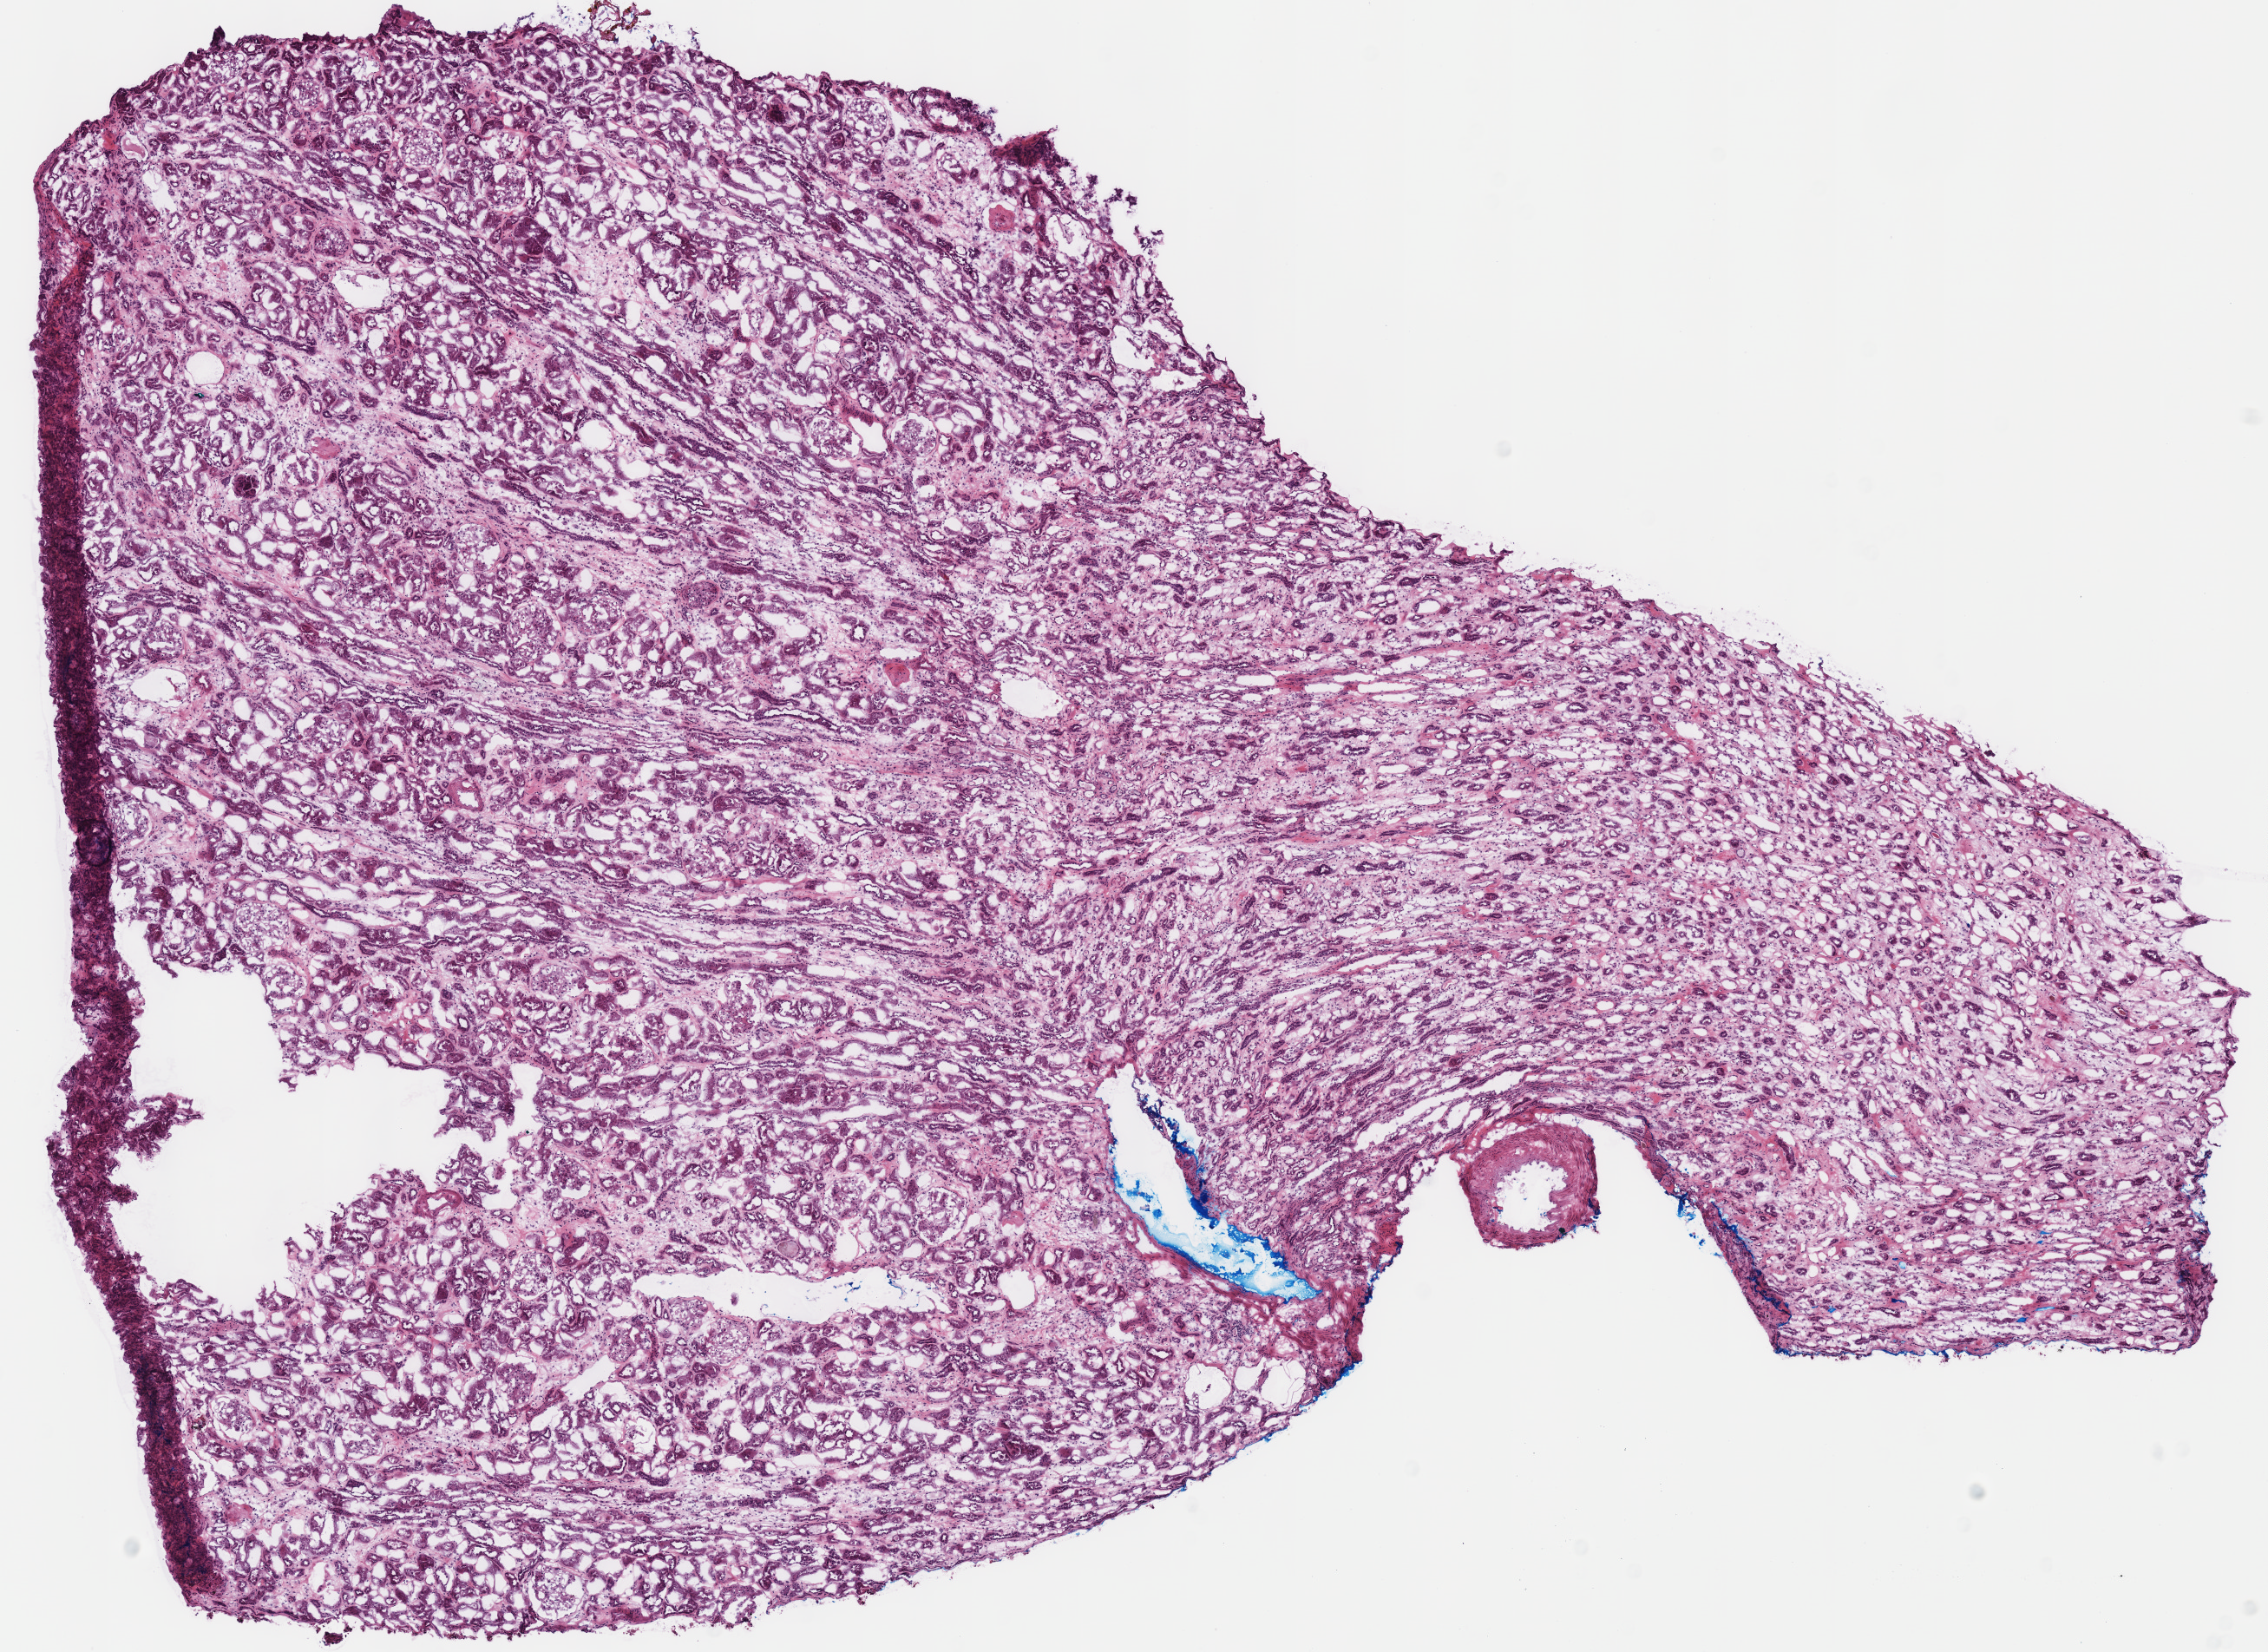
Digitized H&E tissue section (whole slide) — a low-resolution overview of the entire scanned area, about 10.3 x 7.5 mm (slide scanned at 40x), frozen section from the top of the tissue portion, kidney, solid tissue normal (non-tumour tissue) sample. Female patient; age at initial diagnosis 79 years. Composition of this section per pathologist review: tumour cells 0%, tumour nuclei 0%, normal cells 65%, stromal cells 35%, necrosis 0%. Infiltration values recorded for this section: lymphocyte infiltration 10%, monocyte infiltration 3%, neutrophil infiltration 0%.
* this section: solid tissue normal sample (biorepository sample class)
* patient diagnosis: Renal cell carcinoma, chromophobe type